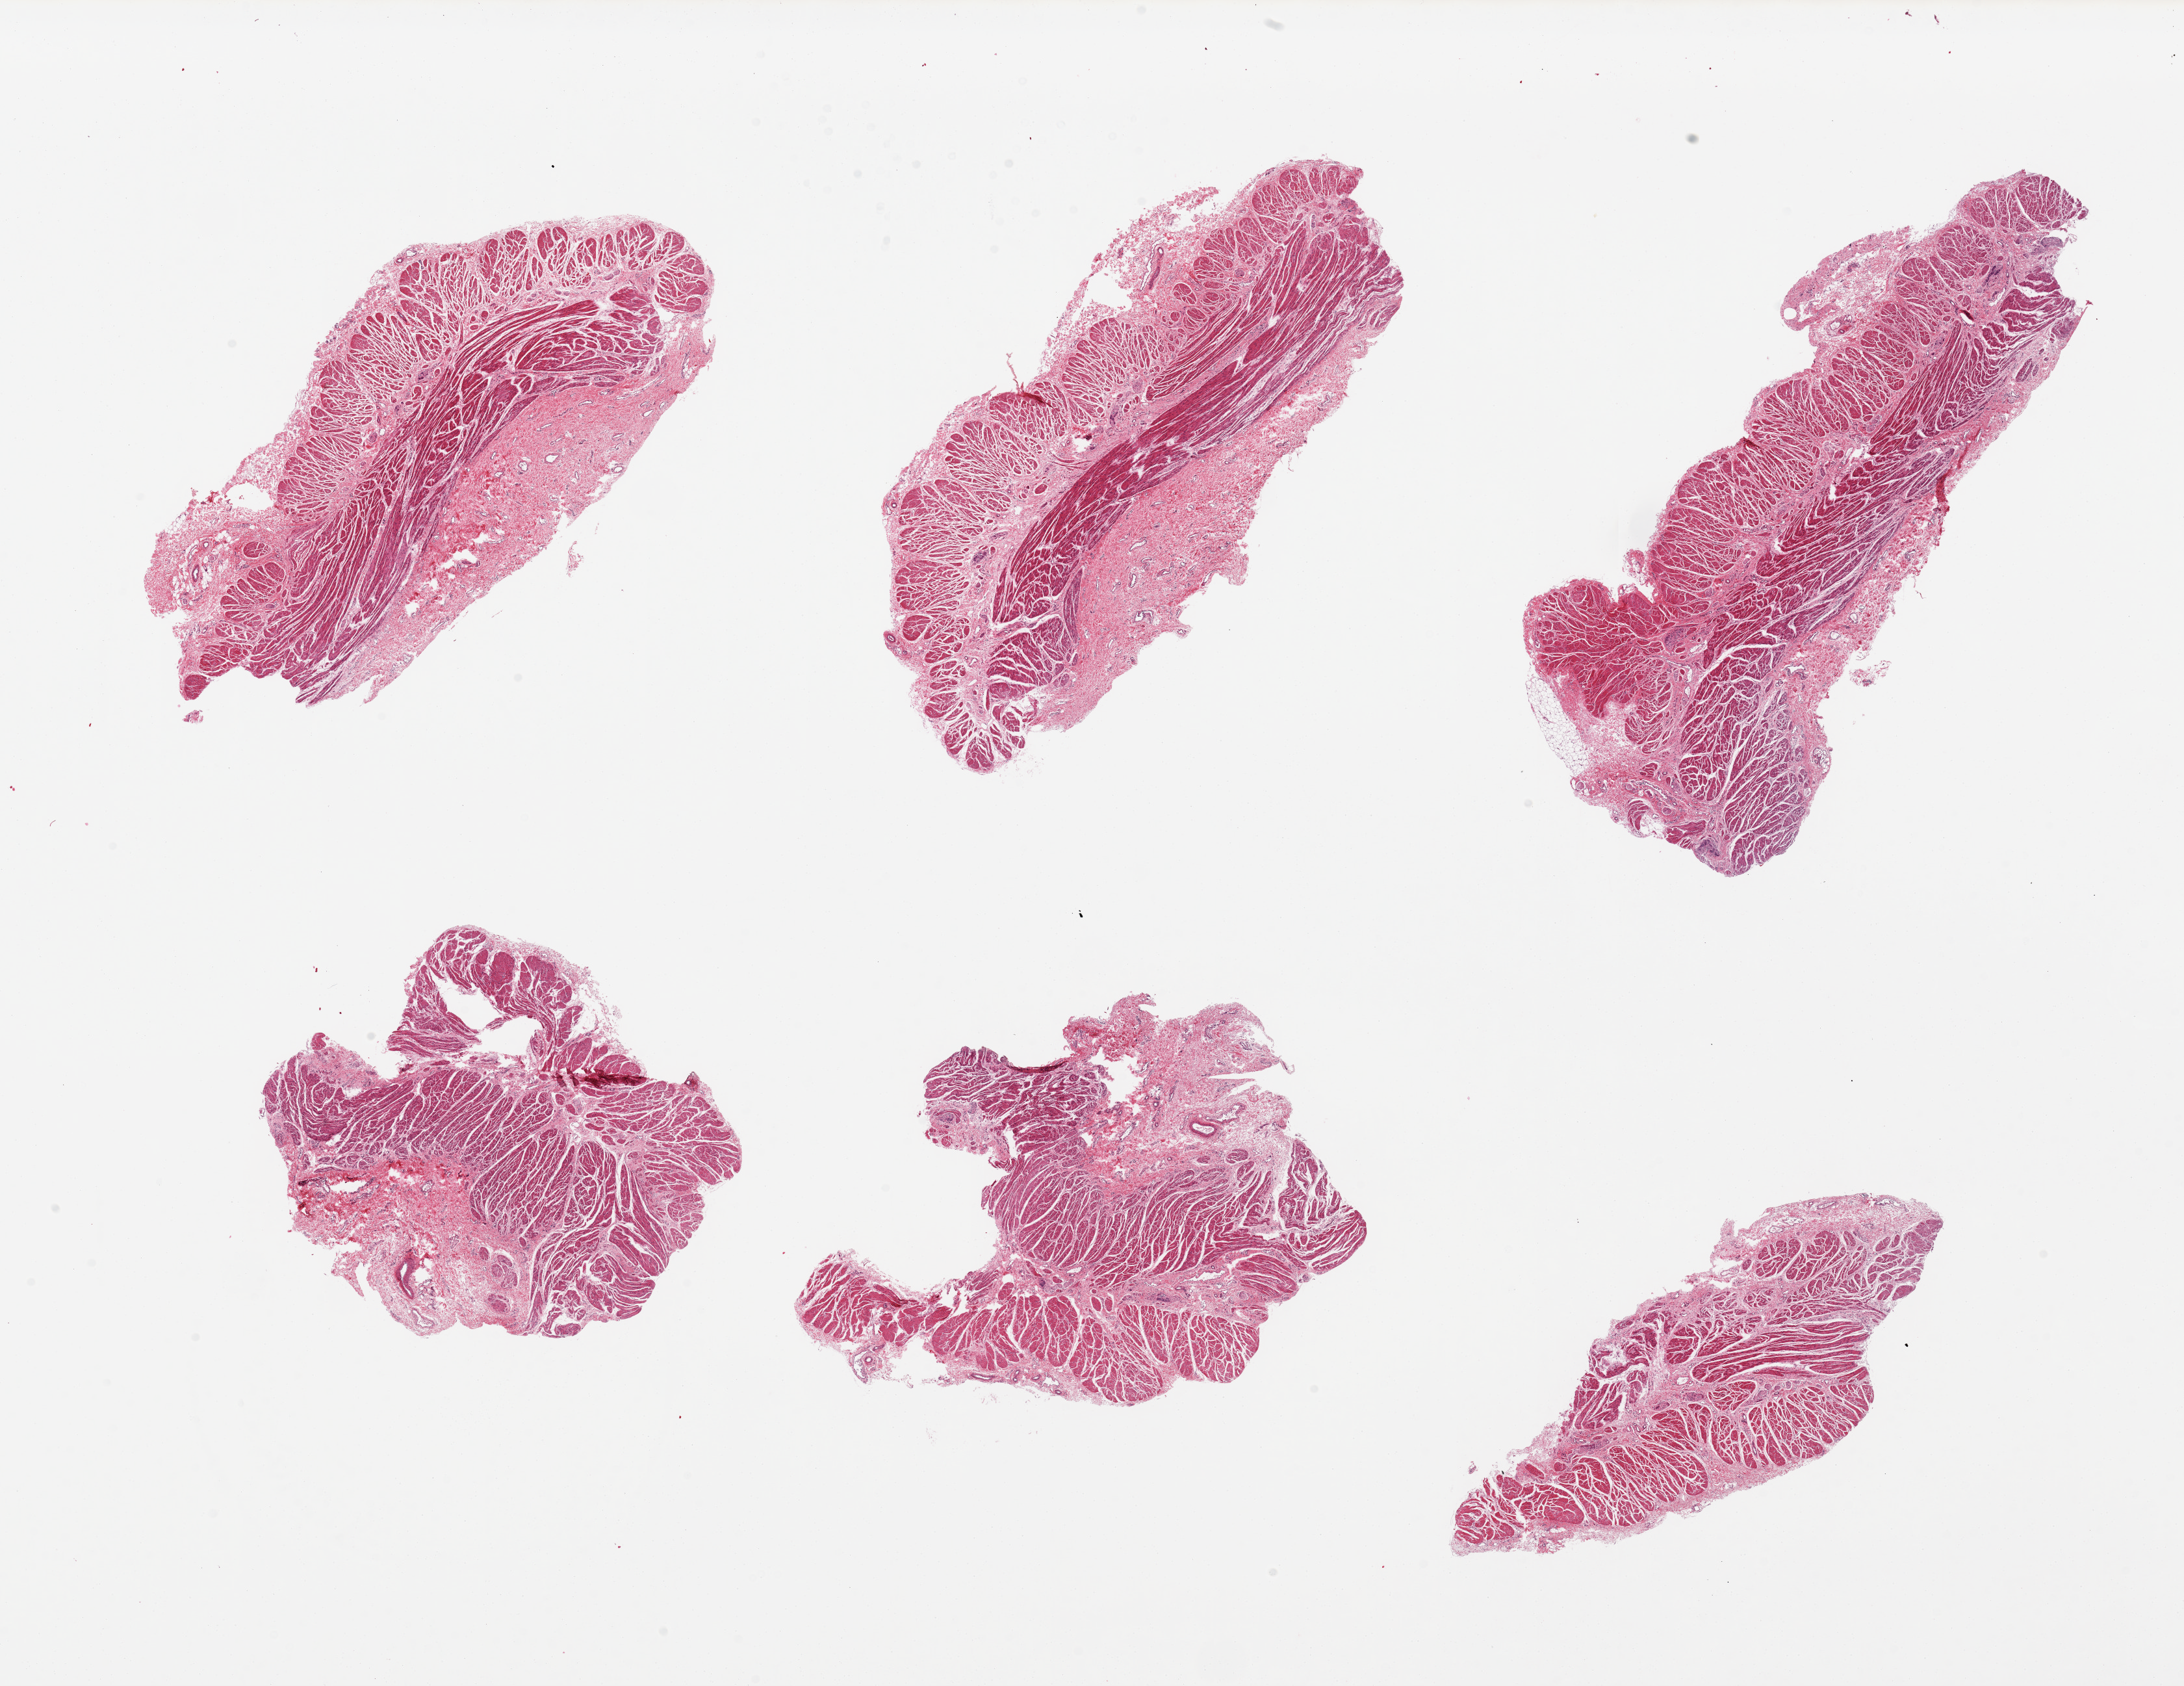
Whole-slide image, haematoxylin and eosin stain, whole scanned area (about 26.6 x 20.5 mm) shown as a low-resolution overview. PAXgene-fixed paraffin-embedded (PFPE) section. Target tissue: gastroesophageal junction. Donor tissue sample. Donor sex: male.
- pathologist's review note for this sample: 6 pieces; all muscularis